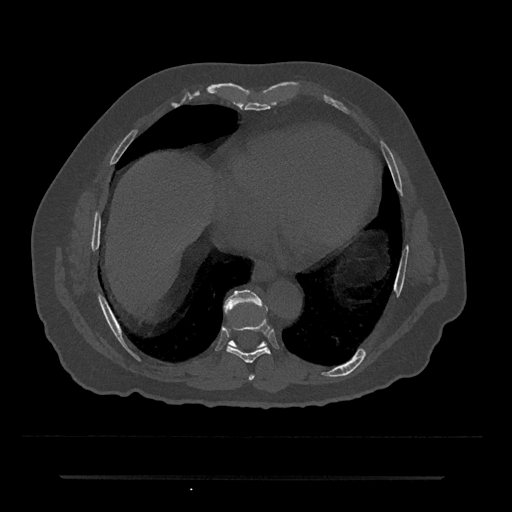
CT including the spine, one axial slice. Slice 317 of 797 in the series (ordered by position). Reconstruction kernel Br40s/3. Bone window (W 1800 / L 400 HU). 0.5 mm slice thickness. 512 × 512 image matrix, field of view 437 × 437 mm. Patient: male, 69 years. From the clinical record (not read from this slice): primary cancer: prostate.
Outlined on this slice (semi-automatic segmentation, software-assisted and operator-edited):
- T7 vertebra: box from (x=249, y=374) to (x=255, y=380) px
- T8 vertebra: (x=226, y=319)–(x=271, y=363)
- T9 vertebra: (x=224, y=290)–(x=264, y=345)